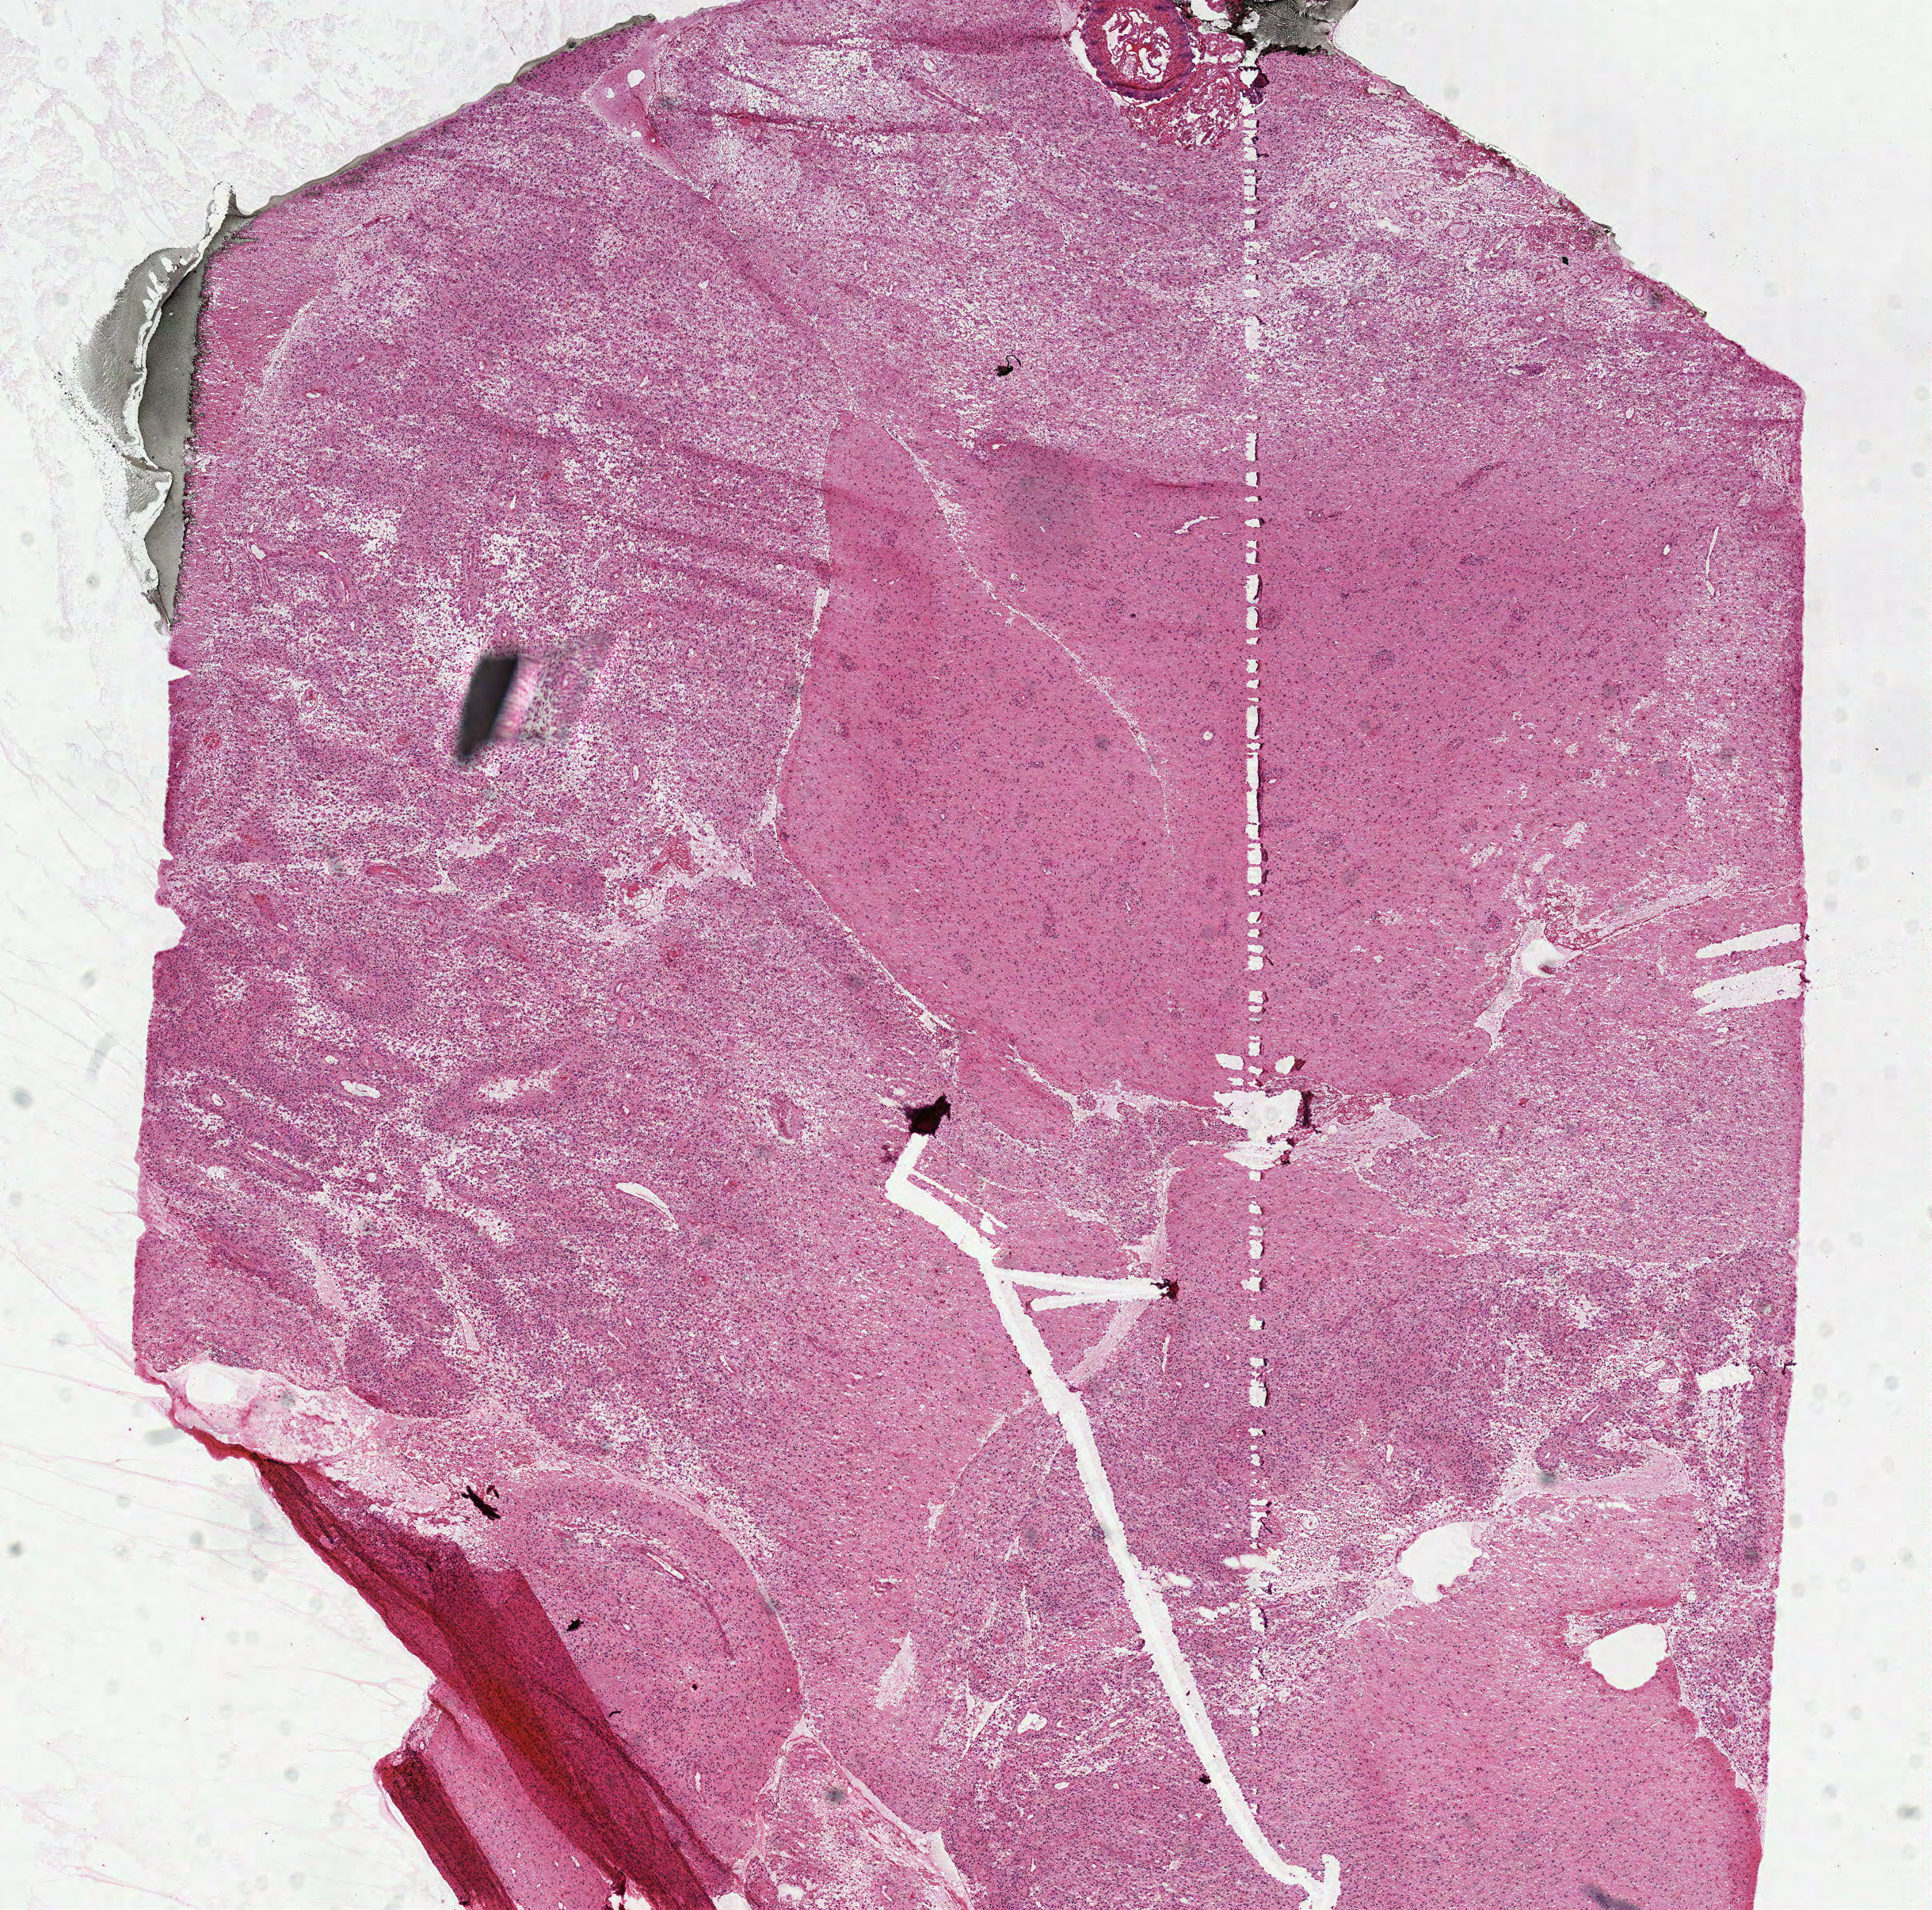
Digitized H&E tissue section (whole slide), low-resolution overview of the scanned area, about 9.6 x 9.5 mm; frozen section from the top of the tissue portion; primary tumour sample from the brain. Female patient; age at initial diagnosis 73 years. Slide review estimates, as recorded: tumour cells 95%, tumour nuclei 75%, normal cells 0%, stromal cells 0%, necrosis 5%.
- diagnosis: Glioblastoma